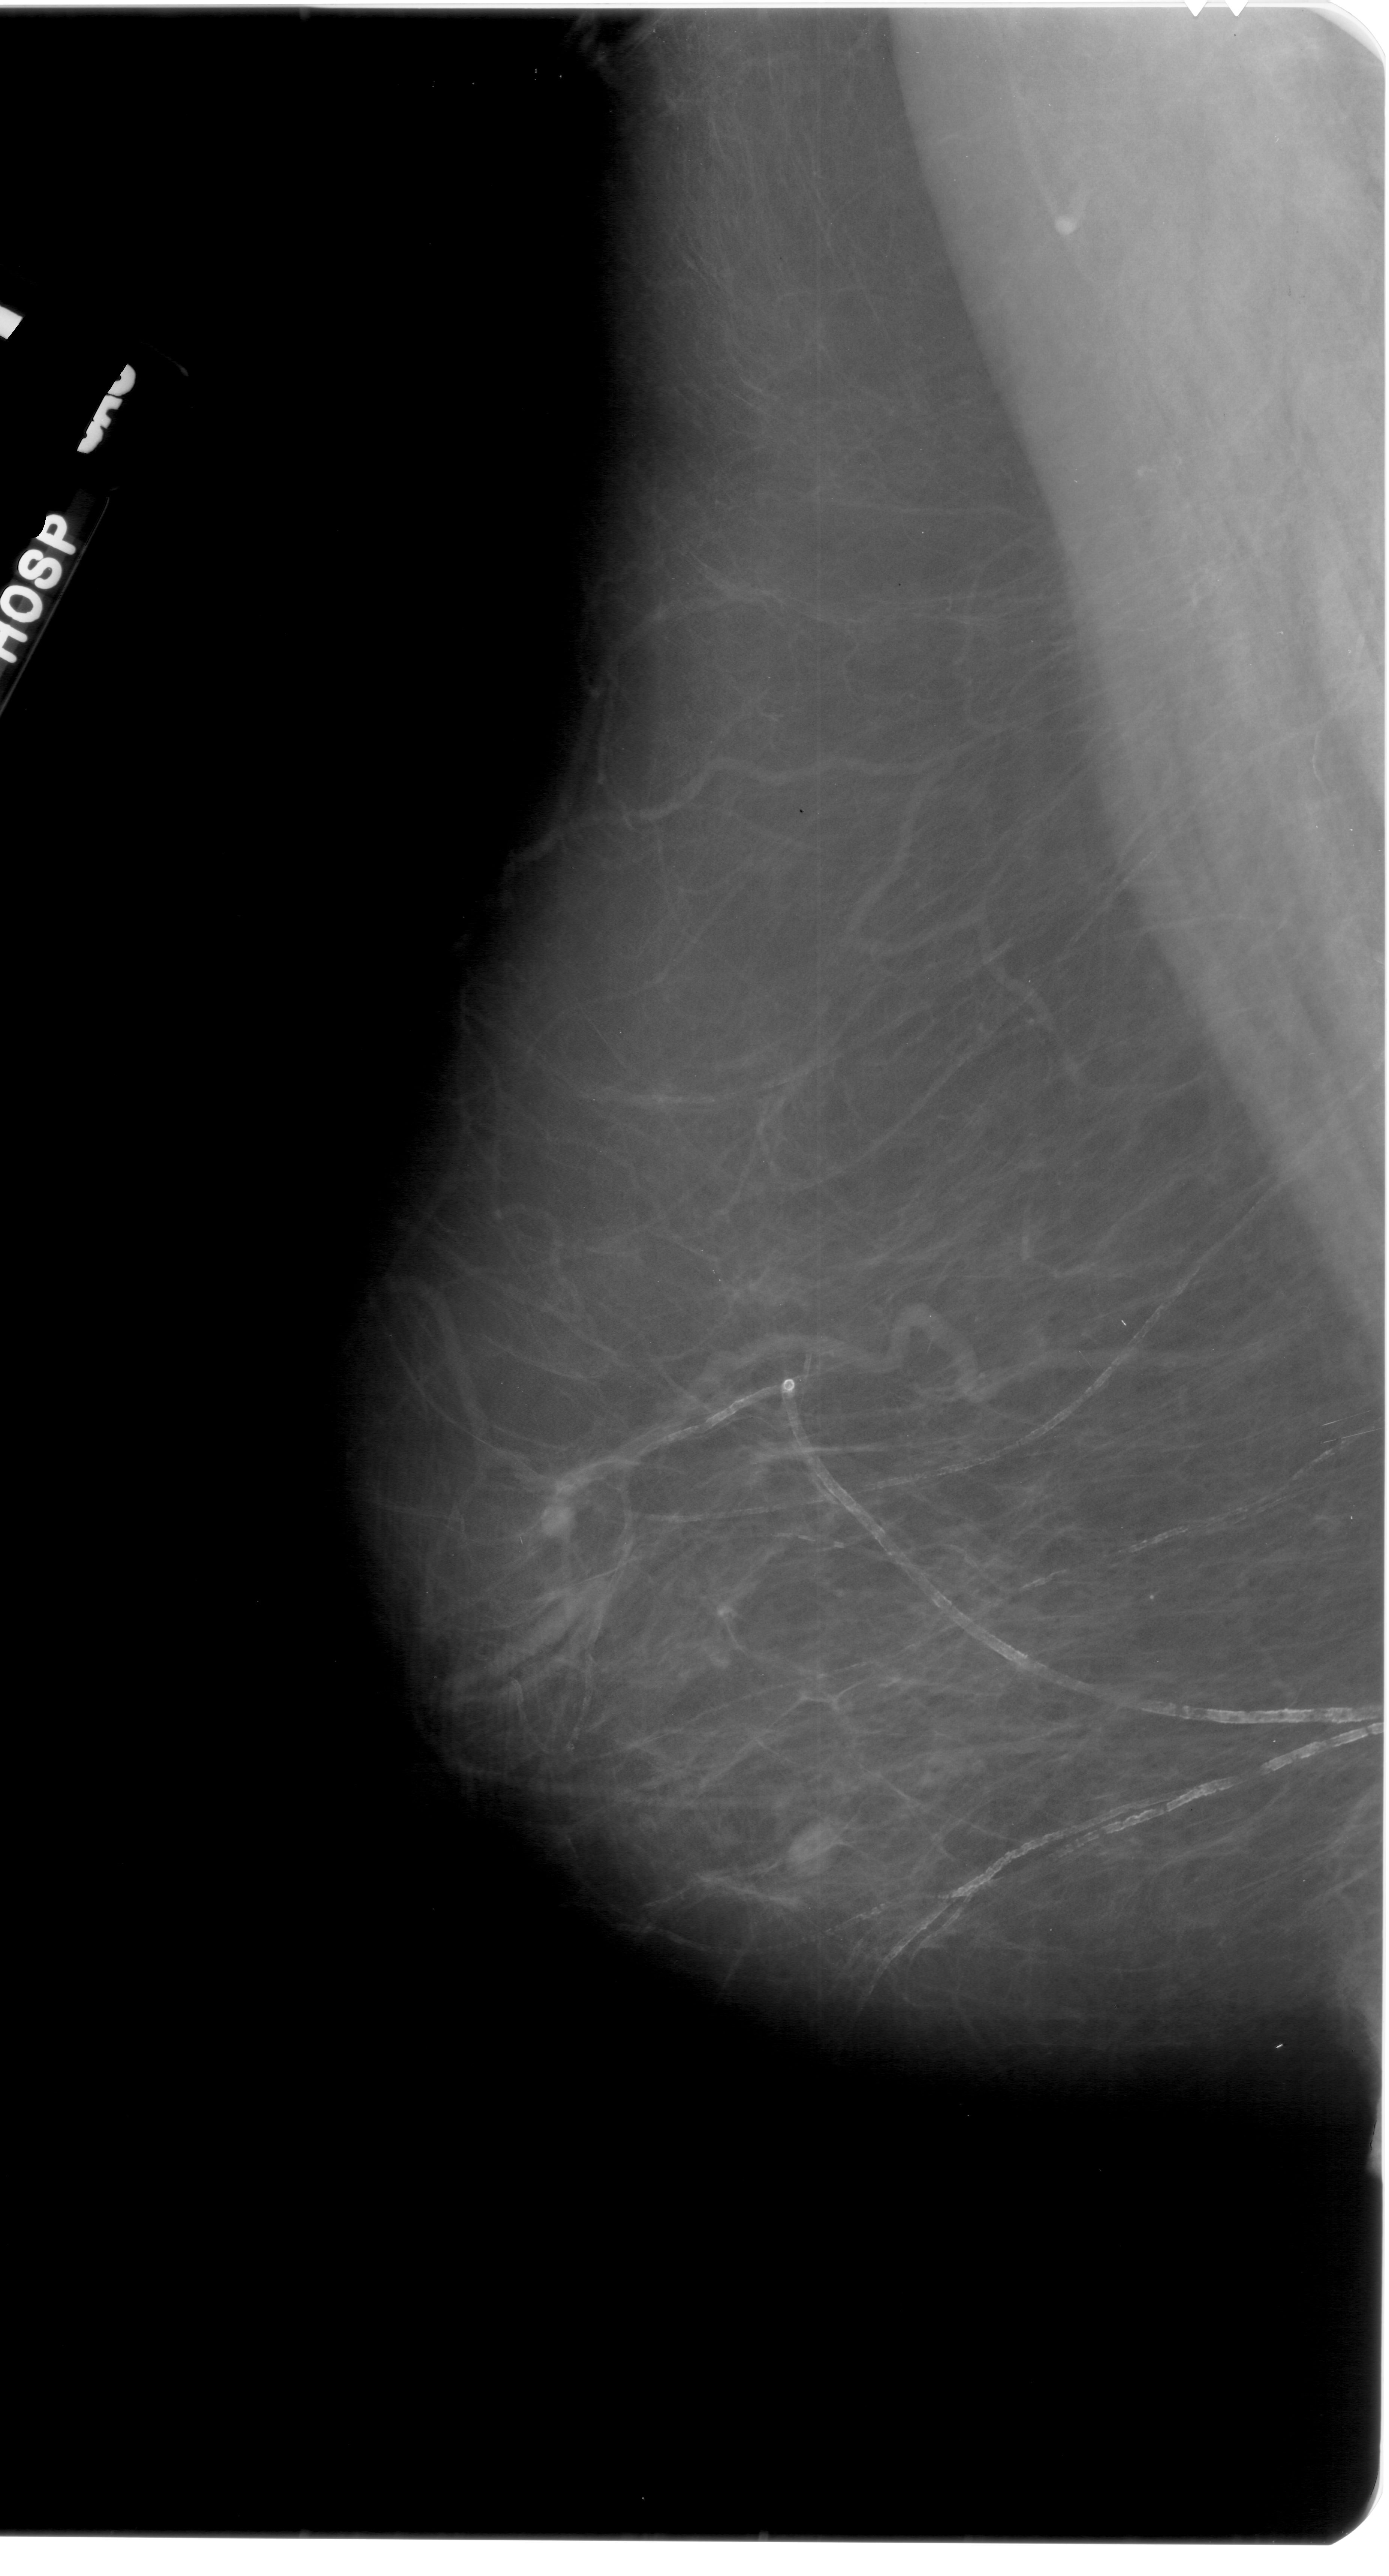
Mammogram (digitized film); left breast; mediolateral oblique (MLO) view; breast composition: scattered fibroglandular densities (BI-RADS density category 2 of 4); 1389 × 2576 image matrix.
Marked abnormalities (boxes around the expert regions of interest):
- mass, shape oval, margins circumscribed; BI-RADS assessment category 4; pathology result (as recorded, not read from the image): malignant: box from (x=526, y=1476) to (x=578, y=1547) px